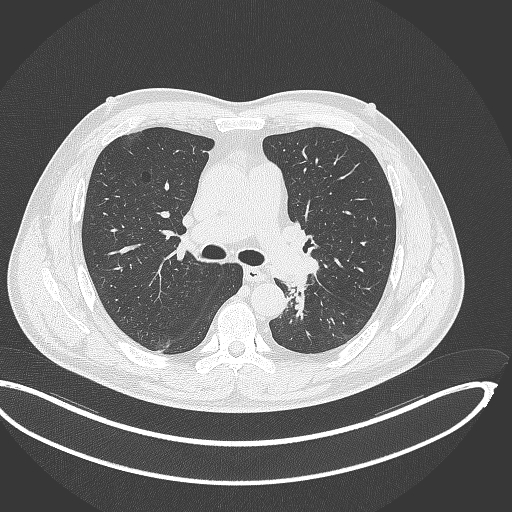
Chest CT, one axial slice; slice 219 of 362 in the series (ordered by position); lung window (W 1500 / L -600 HU); 512 × 512 image matrix, field of view 442 × 442 mm. Male patient, age 50 years. Case-level facts recorded for this patient, not image findings: clinical TNM (as recorded): T2a N3 M0.
Annotated regions visible in this slice (rectangle marked by the reading radiologist):
- lung tumour (recorded histology: squamous cell carcinoma): bounding box (x1, y1, x2, y2) in pixels: (283, 276, 311, 324)